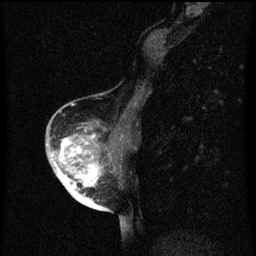
Breast MRI (dynamic contrast-enhanced), one sagittal slice; slice 27 of 60 in the series (ordered by position); dynamic contrast-enhanced series, image 2 of 3 at this slice position (ordered by acquisition); 1.5 T; TE 4.2 ms, TR 8 ms; 2 mm slice thickness; 256 × 256 image matrix. Patient: female, 56 years.
Outlined on this slice (semi-automatic segmentation, software-assisted and operator-edited):
- analysis volume of interest (the breast-tissue region the enhancement analysis was run in; not a lesion): bounding box [x1, y1, x2, y2] px = [54, 124, 120, 199]
- tumour enhancement mask (voxels above the 70 % enhancement threshold inside the analysis volume of interest): [54, 130, 101, 199]